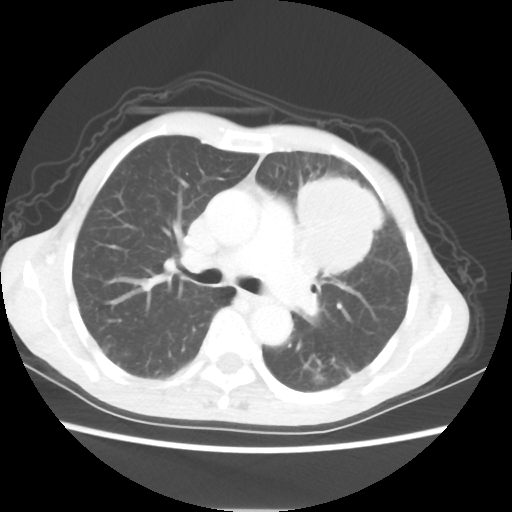
Chest CT, one axial slice. Position 37 of 56 along the scan axis. Lung window (W 1500 / L -600 HU). 5 mm slice thickness. 512 × 512 image matrix, field of view 331 × 331 mm. Female patient, age 60 years. Case-level facts recorded for this patient, not image findings: clinical TNM (as recorded): T4 N1 M0.
Structures marked on this image (rectangle marked by the reading radiologist):
- lung tumour (recorded histology: adenocarcinoma): bounding box [x1, y1, x2, y2] px = [291, 171, 383, 280]